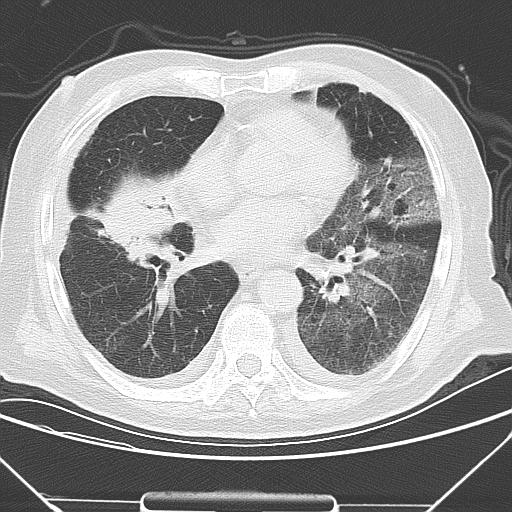
Chest CT, one axial slice; position 14 of 43 along the scan axis; 120 kVp; lung window (W 1500 / L -600 HU); 512 × 512 image matrix. Male patient, age 85 years. From the clinical record (not read from this slice): clinical TNM (as recorded): T4 N3 M2.
Outlined on this slice (bounding box drawn by a radiologist):
- lung tumour (recorded histology: squamous cell carcinoma): bounding box (x1, y1, x2, y2) in pixels: (106, 166, 180, 258)